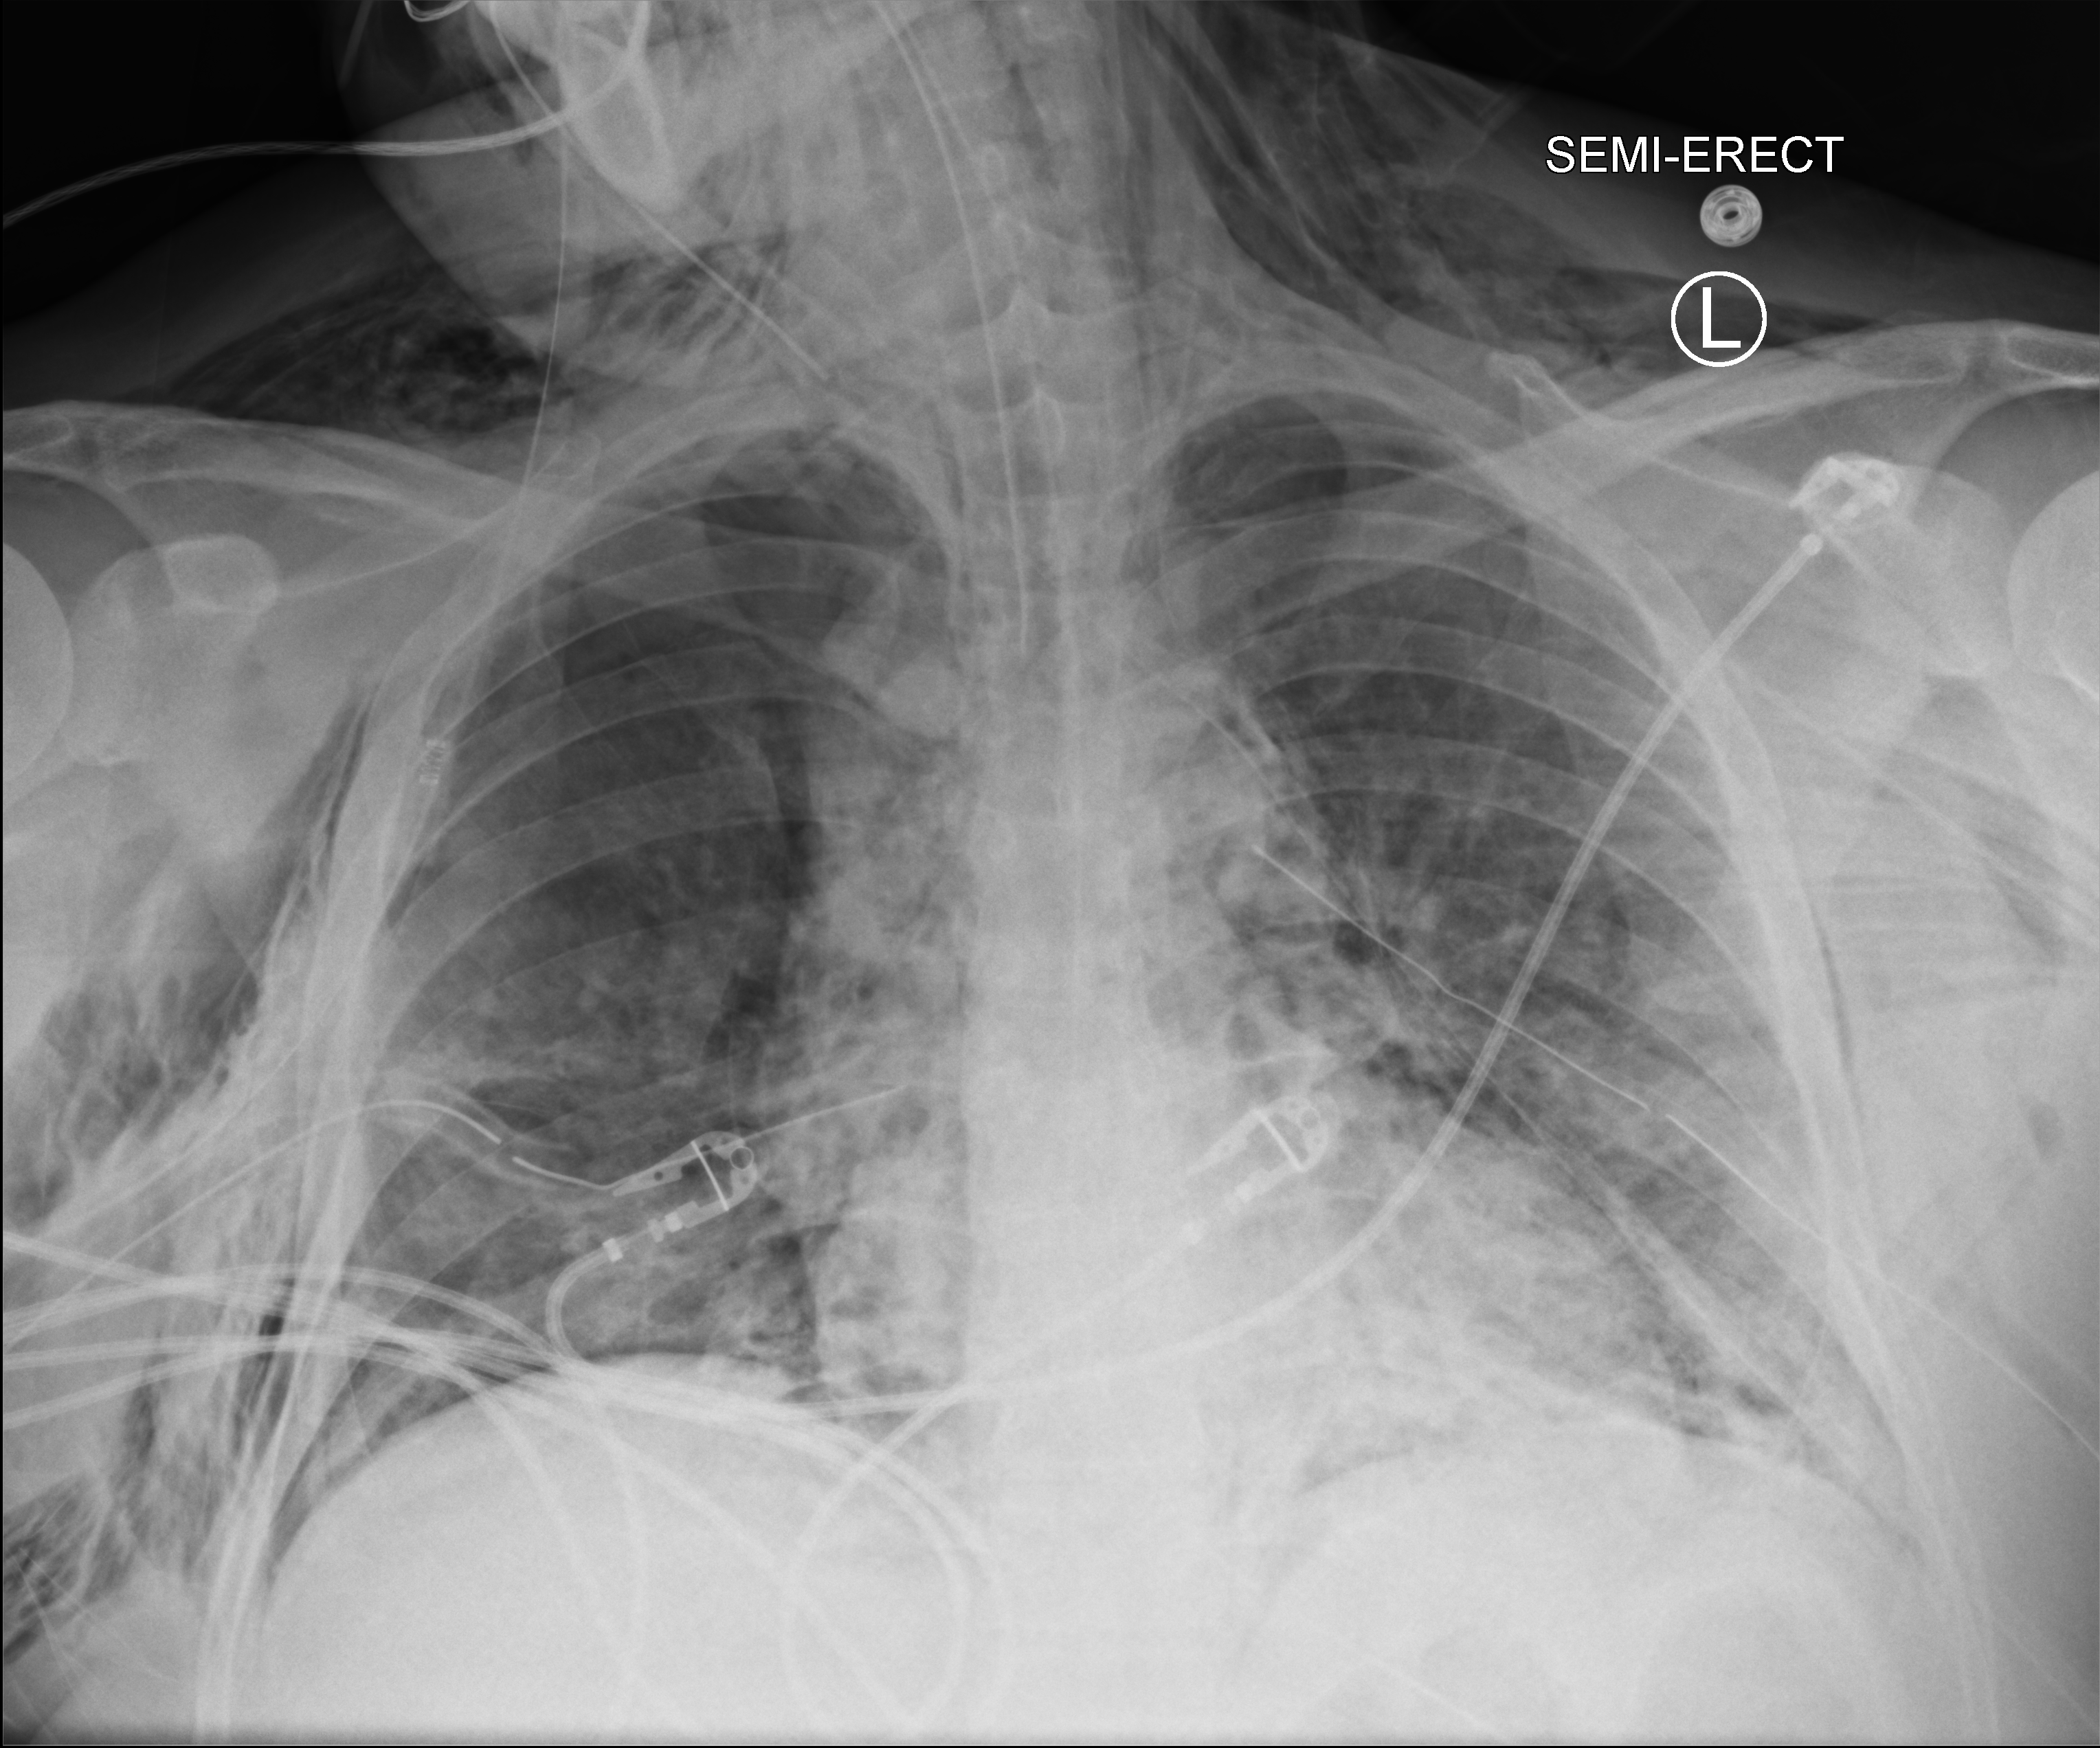
Bedside chest radiograph (computed radiography); anteroposterior (AP) projection. Patient hospitalised with COVID-19; male, aged 18–59 years.
Hospital-stay facts (about this admission, not read from this image; timing relative to this image not recorded): chronic kidney disease (admission record): no; other chronic lung disease (admission record): no; mechanically ventilated during this hospital stay: yes.